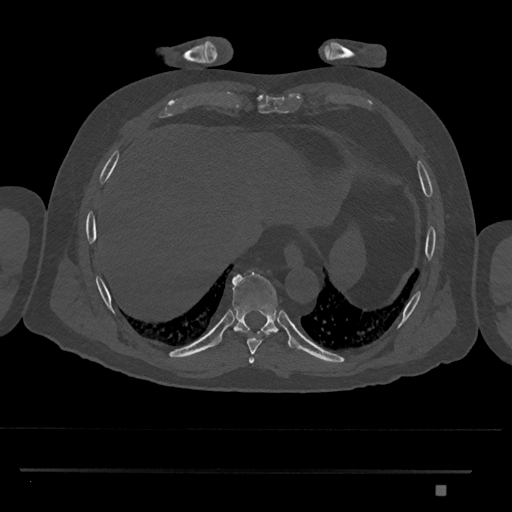
CT including the spine, one axial slice; slice 1079 of 1134 in the series (ordered by position); reconstruction kernel Br40s/3; 120 kVp; bone window (W 1800 / L 400 HU); 512 × 512 image matrix. Patient: male, 65 years. From the clinical record (not read from this slice): primary cancer: prostate.
Outlined on this slice (semi-automatically segmented with operator editing):
- T8 vertebra: bounding box (x1, y1, x2, y2) in pixels: (247, 332, 274, 356)
- T9 vertebra: (221, 270, 289, 345)